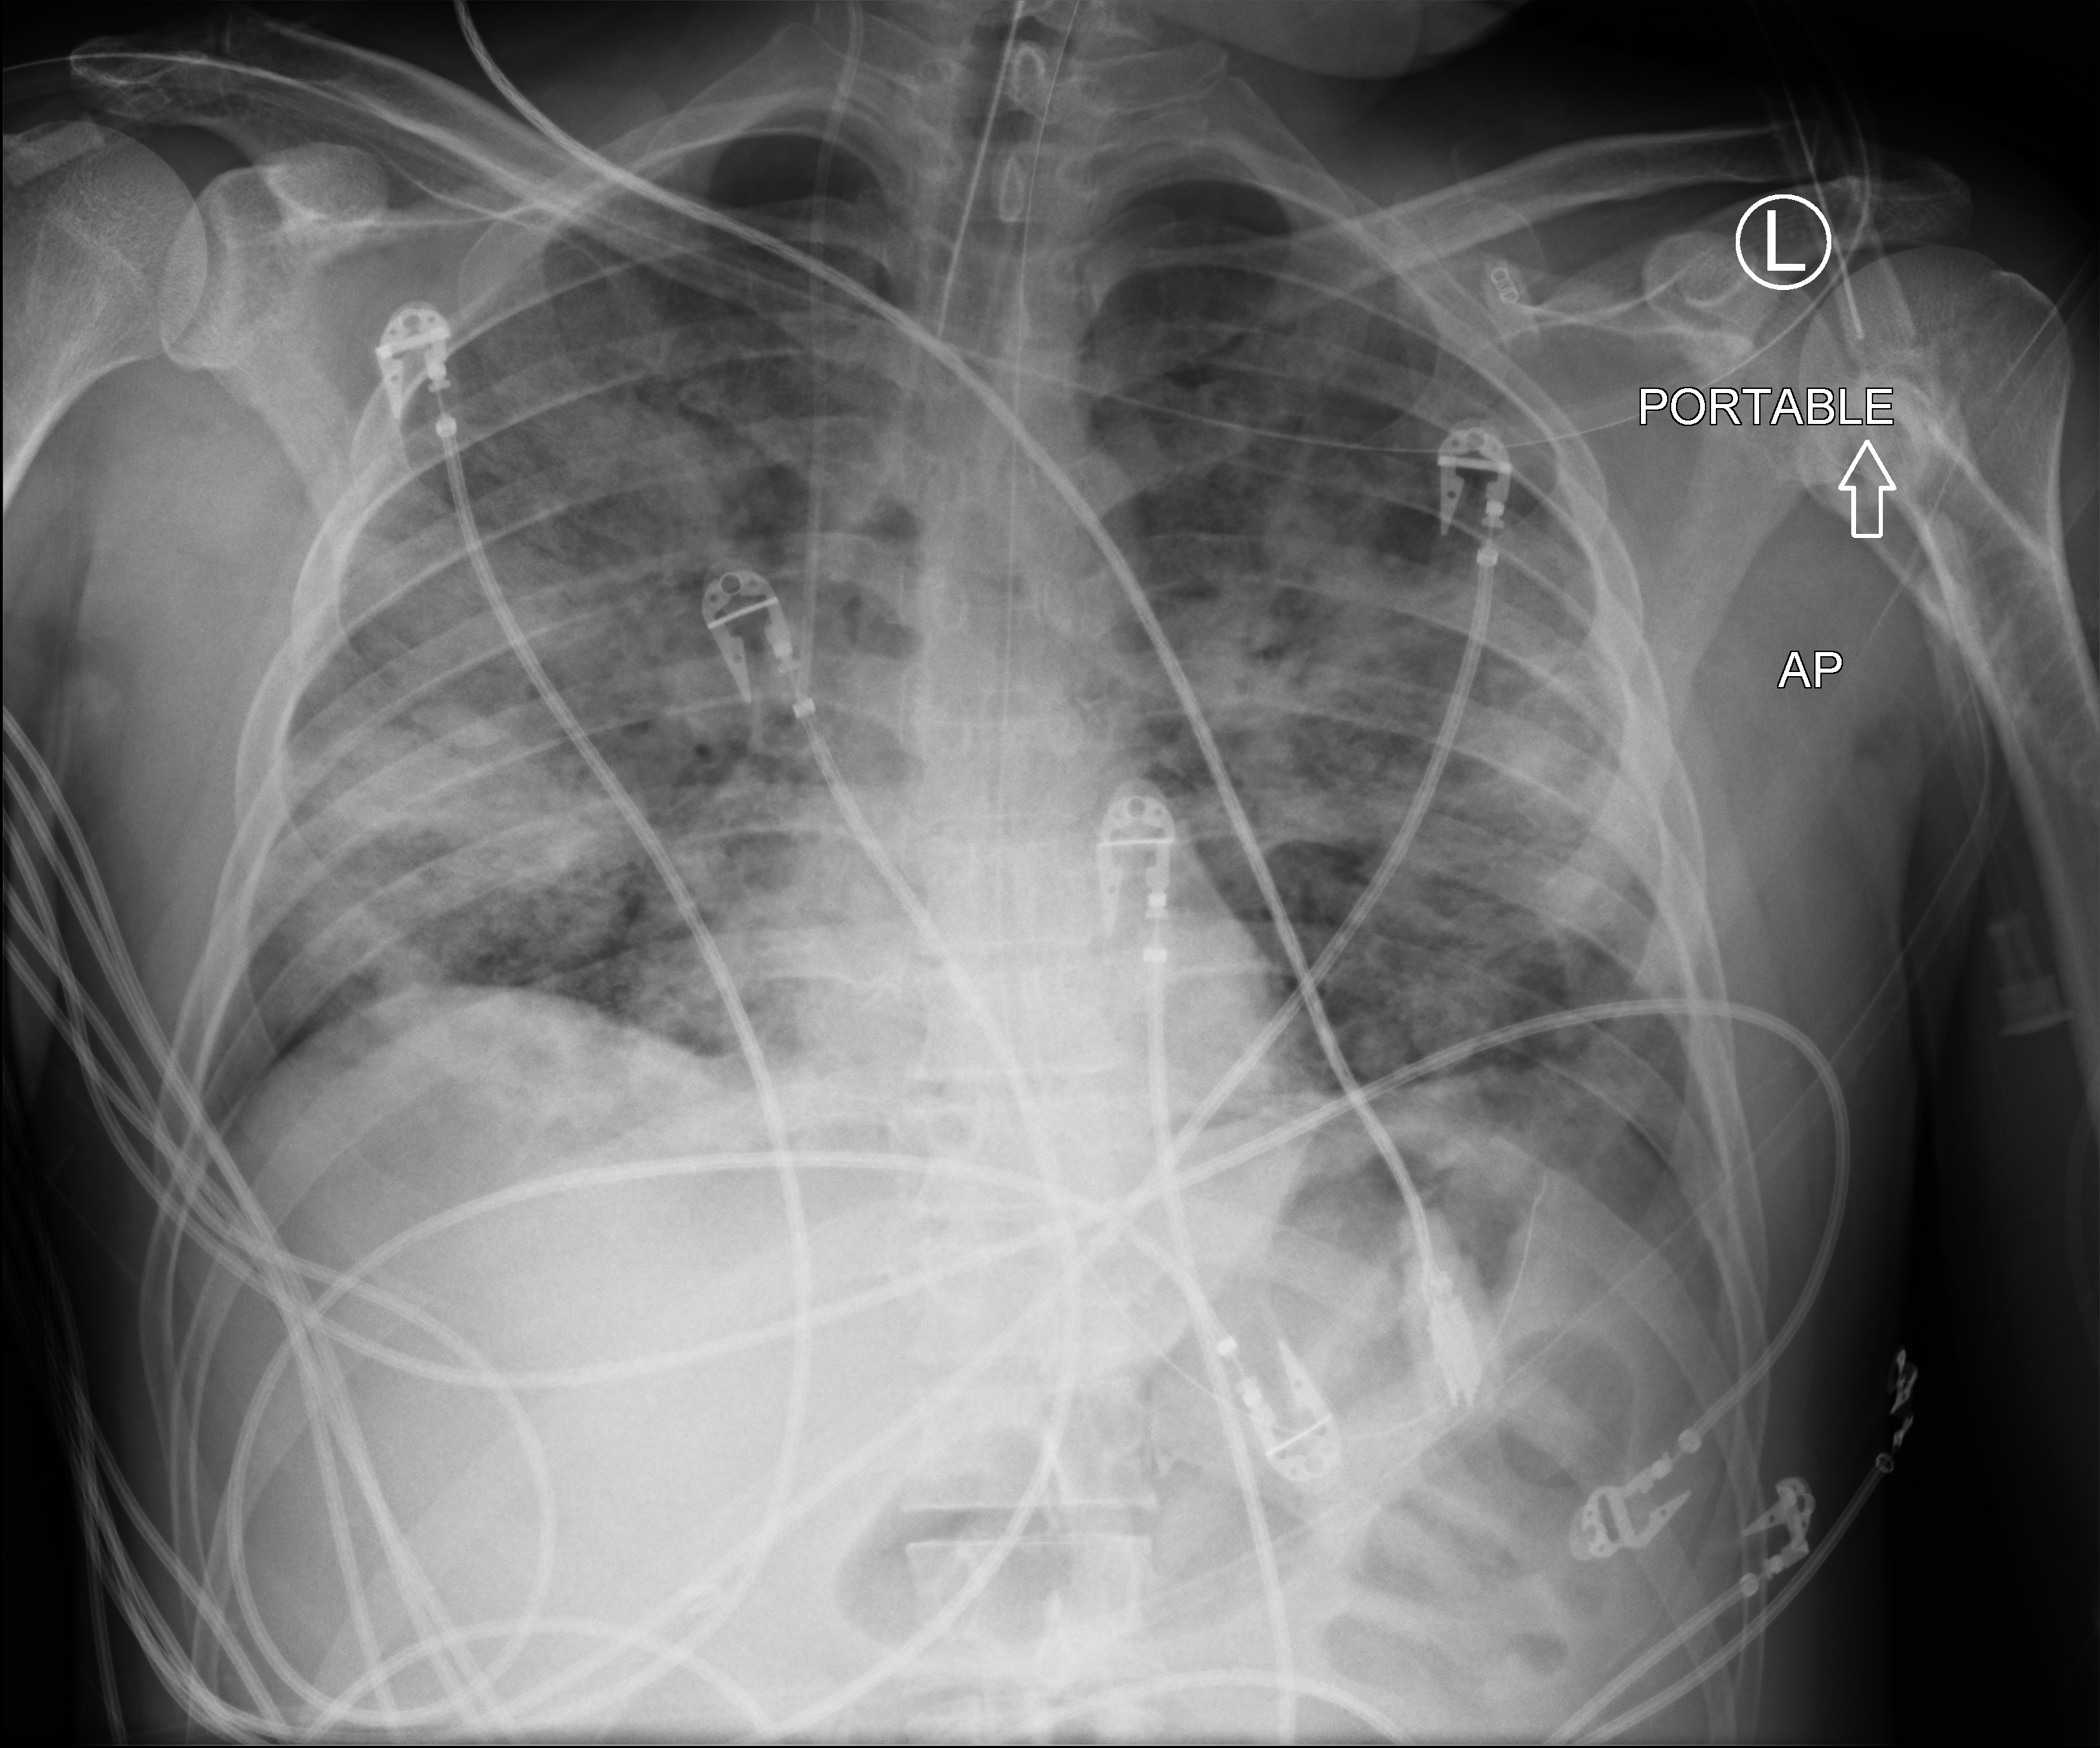
Chest X-ray (portable). Patient hospitalised with COVID-19; male, aged 18–59 years.
Admission-level facts for this patient (not findings on this image; timing relative to this image not recorded): admitted to intensive care during this hospital stay: yes.